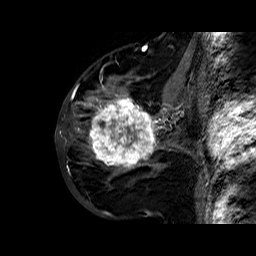
Breast MRI (dynamic contrast-enhanced), one sagittal slice. Position 27 of 60 along the scan axis. Dynamic contrast-enhanced series, time point 2 of 6 at this slice position (early post-contrast). 1.5 T. TE 6.4 ms, TR 32.8 ms. 256 × 256 image matrix. Female patient. Case-level facts recorded for this patient, not image findings: setting: breast cancer imaged before/during neoadjuvant chemotherapy; receptor status: HR-positive, HER2-negative.
Structures marked on this image (semi-automatic segmentation, software-assisted and operator-edited):
- analysis volume of interest (the breast-tissue region the enhancement analysis was run in; not a lesion): bounding box (x1, y1, x2, y2) in pixels: (86, 77, 163, 177)
- tumour enhancement mask (voxels above the 100 % enhancement threshold inside the analysis volume of interest): (88, 84, 163, 169)